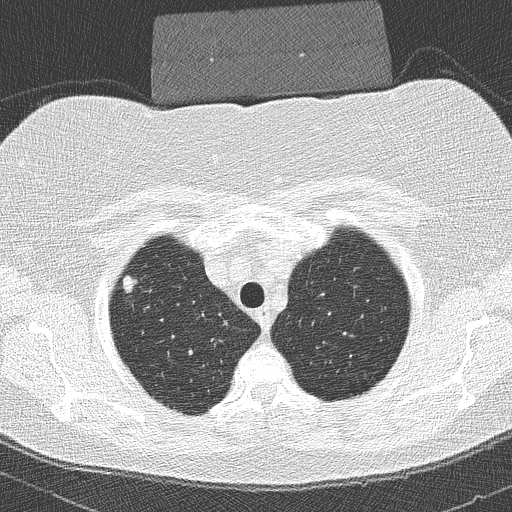
Low-dose screening chest CT, axial slice. Second annual screen. Lung window (W 1500 / L -600 HU). Lung (sharp) reconstruction kernel (B50f). Slice 36 of 293 in the series. Female participant, aged 58 years at enrolment.
Expert-annotated lung lesion, bounding box [x1, y1, x2, y2] px = [111, 270, 150, 307]. The screening reader recorded 2 non-calcified nodules or masses ≥4 mm on this exam (right upper lobe, right upper lobe); which of them this box marks is not recorded. Later outcome: lung cancer diagnosed 447 days after this screen (after the third annual screen) — bronchiolo-alveolar adenocarcinoma, NOS, right upper lobe, well differentiated (G1), stage IA (AJCC 6th edition), 9 mm at pathology.